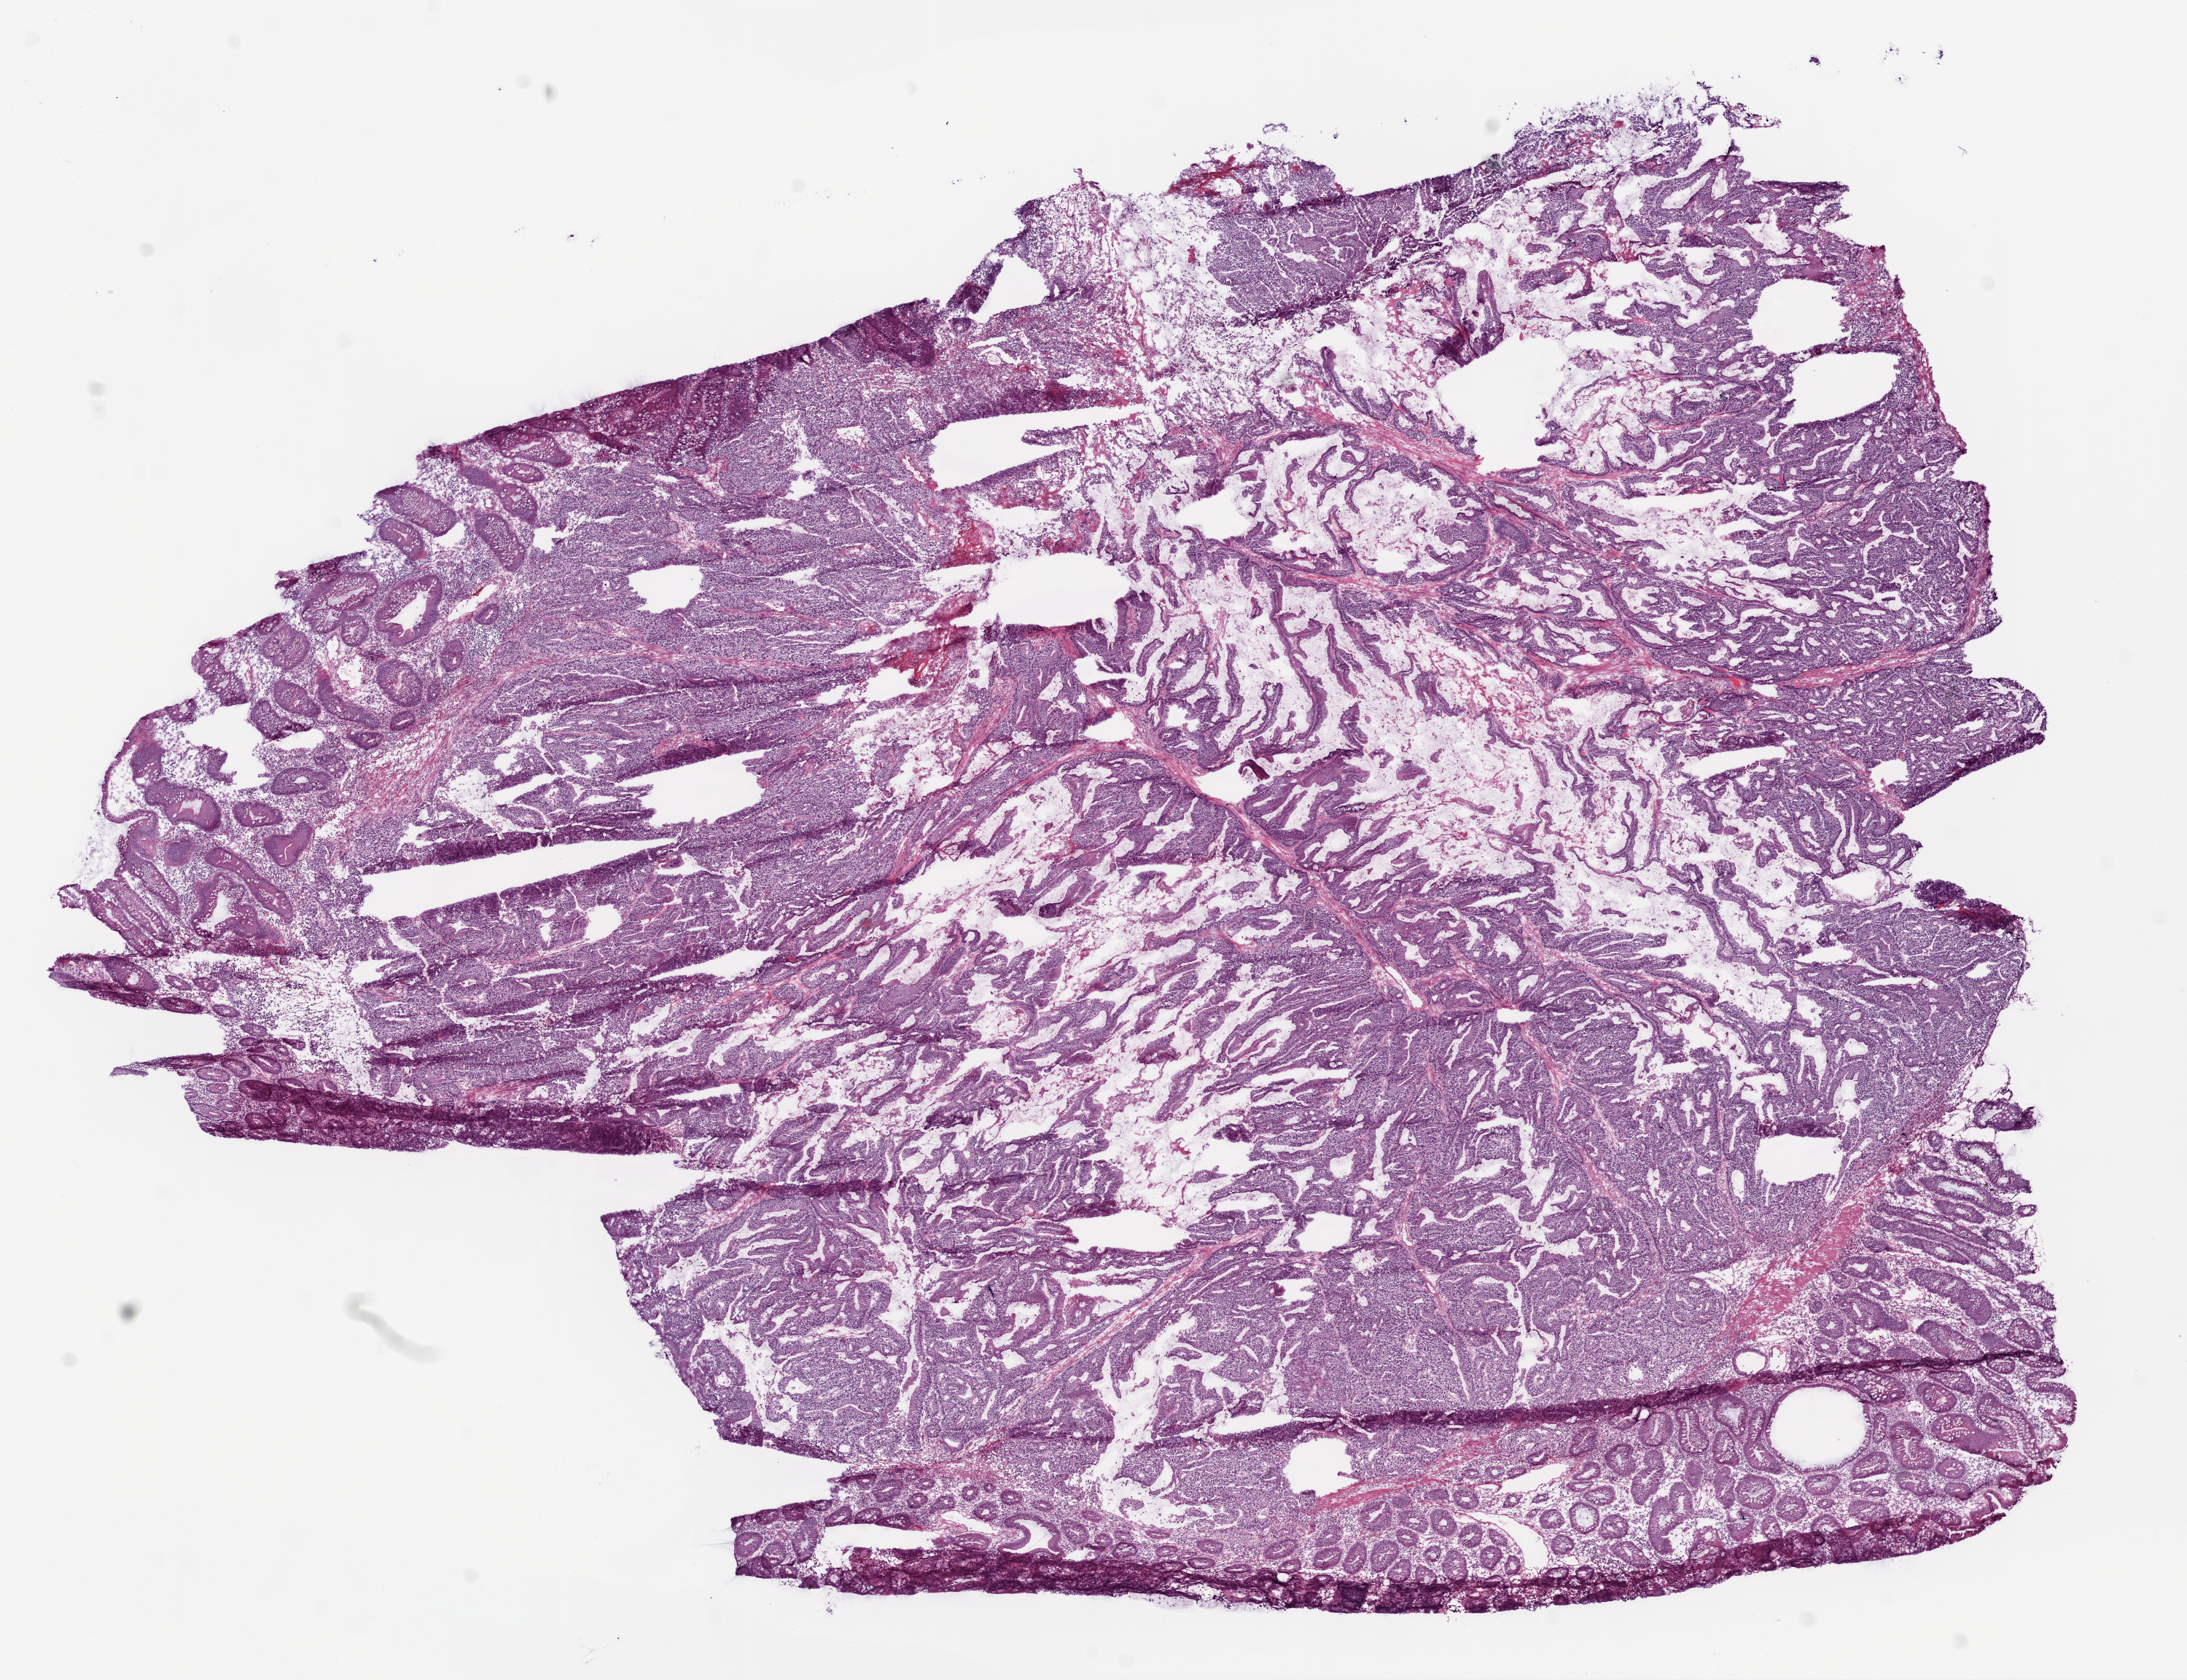
H&E-stained whole-slide image — shown as a low-resolution overview of the whole scanned area (about 12.0 x 9.2 mm, acquisition: 20x scan), frozen section, primary tumour sample from the colon. Patient sex: male. Pathologist review of this section (percent, as recorded): tumour cells 80%, tumour nuclei 80%, normal cells 10%, stromal cells 10%, necrosis 0%.
TNM: T3 N1 M0. AJCC pathologic stage: IIIB (6th edition). Pathologic diagnosis: Adenocarcinoma, NOS (ascending colon).